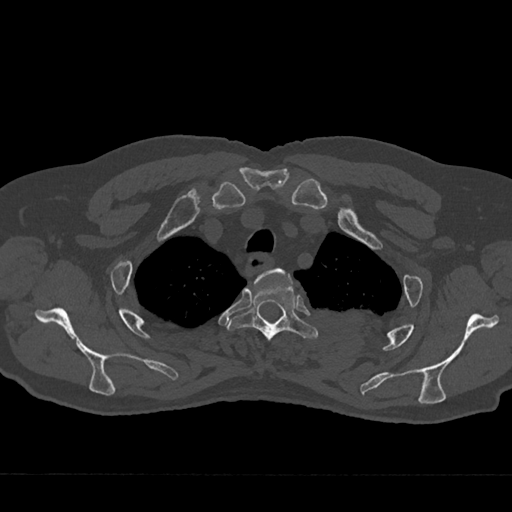
CT including the spine, one axial slice; slice 576 of 797 in the series (ordered by position); reconstruction kernel Br40s/3; 120 kVp; bone window (W 1800 / L 400 HU); 512 × 512 image matrix, field of view 377 × 377 mm. Male patient, age 75 years. From the clinical record (not read from this slice): primary cancer: renal.
Outlined on this slice (semi-automatically segmented with operator editing):
- T2 vertebra: bounding box <255,268,290,283> (left, top, right, bottom; pixels)
- T3 vertebra: <229,281,317,340>